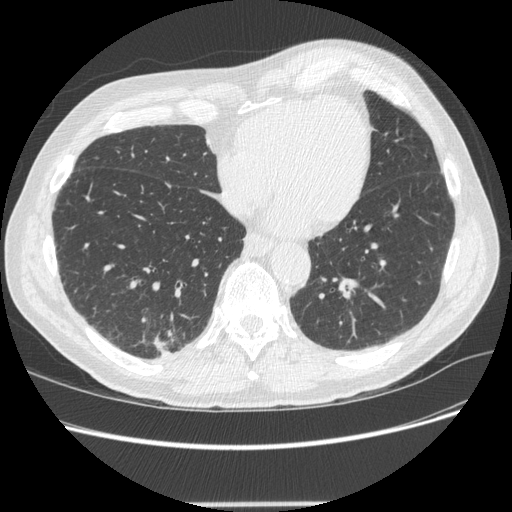
Low-dose screening chest CT, one axial slice; lung window (W 1500 / L -600 HU); 512 × 512 image matrix.
Annotated regions visible in this slice (manually delineated by an expert):
- lesion 1 (tumor, lower lobe of right lung): bounding box (x1, y1, x2, y2) in pixels: (152, 332, 174, 355)